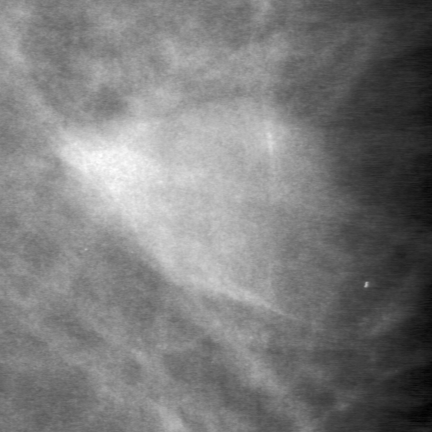
Region of interest cut from a scanned film mammogram (one marked finding); left breast; MLO view.
- Finding: mass, shape lobulated, margins obscured; BI-RADS assessment category 0 (incomplete: needs additional imaging); subtlety rating 5 on a 1 (subtle) to 5 (obvious) scale; pathology (as recorded): benign.